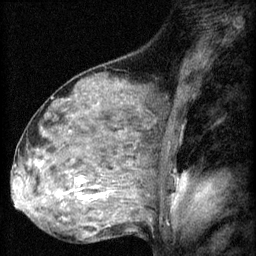
Breast MRI (dynamic contrast-enhanced), one sagittal slice; slice 38 of 60 in the series (ordered by position); 3 images stored at this slice position (order not interpretable as contrast timing); 1.5 T; TE 4.2 ms, TR 8.2 ms; 2 mm slice thickness; 256 × 256 image matrix. Female patient, age 48 years.
Structures marked on this image (semi-automatic segmentation, software-assisted and operator-edited):
- analysis volume of interest (the breast-tissue region the enhancement analysis was run in; not a lesion): bounding box (x1, y1, x2, y2) in pixels: (48, 160, 125, 217)
- tumour enhancement mask (voxels above the 70 % enhancement threshold inside the analysis volume of interest): (74, 180, 84, 183)